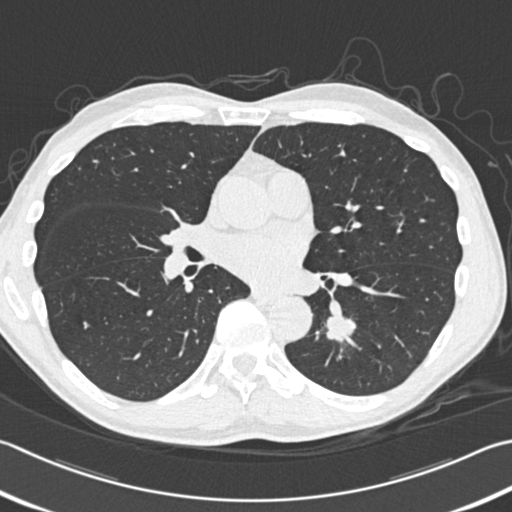
Low-dose screening chest CT, one axial slice; slice 179 of 354 in the series (ordered by position); reconstruction kernel B30f; 120 kVp; lung window (W 1500 / L -600 HU); 512 × 512 image matrix.
Outlined on this slice (outlined manually by an expert reader):
- lesion 1 (tumor, lower lobe of left lung): box from (x=326, y=315) to (x=356, y=342) px